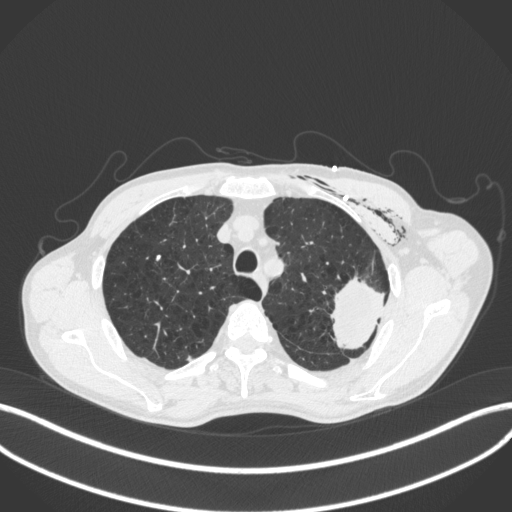
Chest CT, one axial slice. Slice 324 of 416 in the series (ordered by position). 120 kVp. Lung window (W 1500 / L -600 HU). 512 × 512 image matrix. Male patient, age 58 years. Case-level facts recorded for this patient, not image findings: clinical TNM (as recorded): T3 N0 M0.
Structures marked on this image (bounding box drawn by a radiologist):
- lung tumour (recorded histology: adenocarcinoma): bounding box (x1, y1, x2, y2) in pixels: (330, 271, 390, 357)